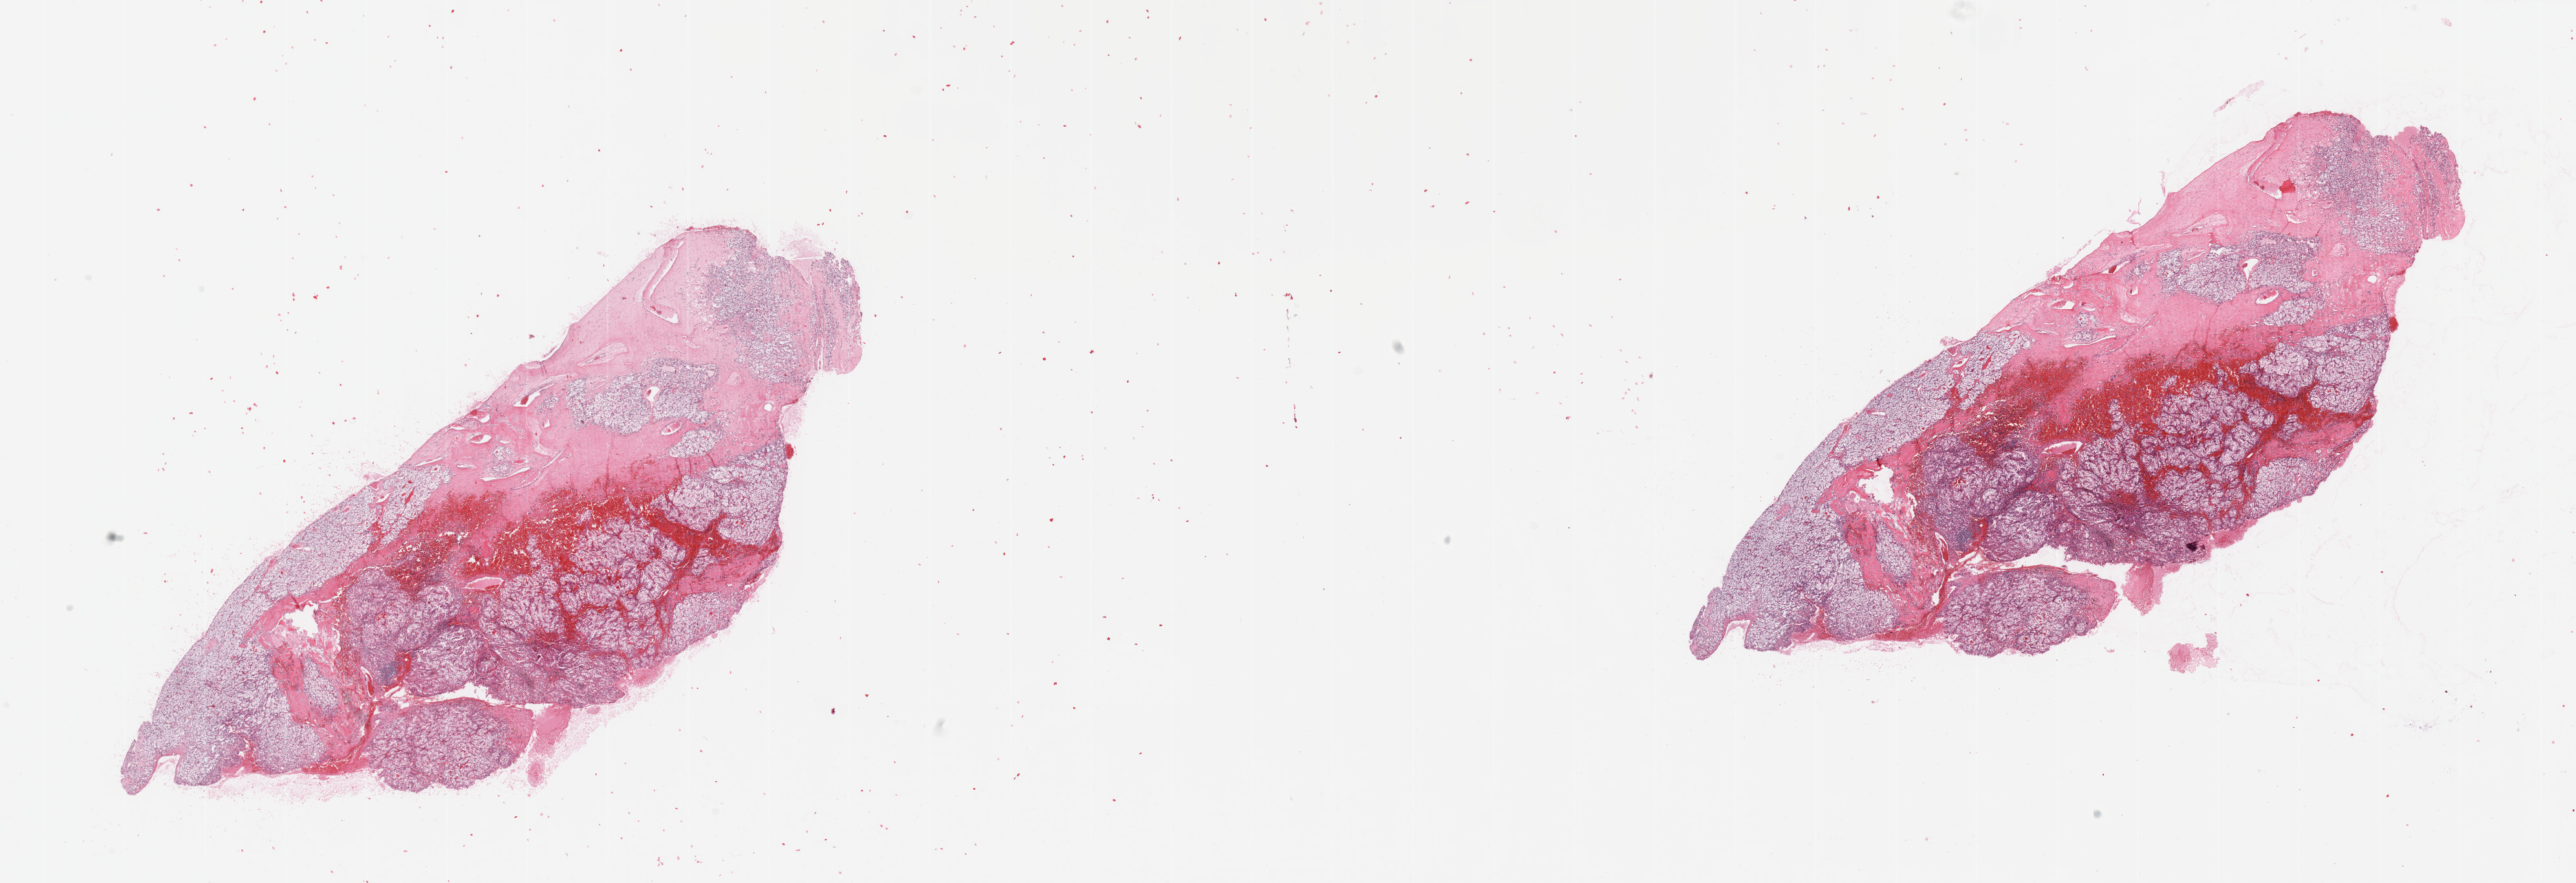
H&E-stained whole-slide image, a low-resolution overview of the entire scanned area, about 31.5 x 10.8 mm (slide scanned at 20x). Tumour tissue sample, sampled site: kidney. Male, 57 y/o. Histologic grade: G3 (poorly differentiated). Composition of this section per pathologist review: tumour nuclei 80%, necrosis 5%.
AJCC pathologic stage: III. Diagnosis: Renal cell carcinoma, NOS.